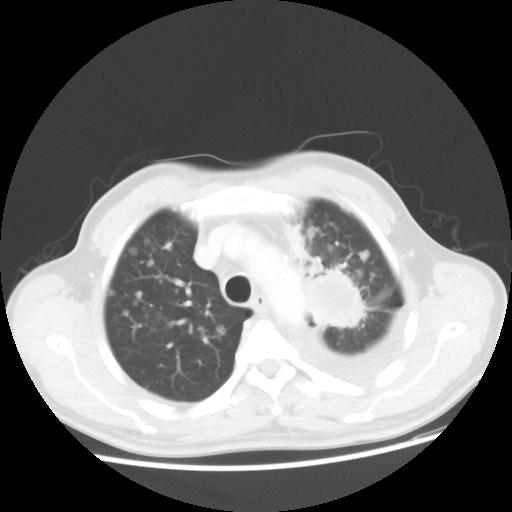
Chest CT, one axial slice. Position 37 of 48 along the scan axis. Reconstruction kernel STANDARD. 100 kVp. Lung window (W 1500 / L -600 HU). 5 mm slice thickness. 512 × 512 image matrix, field of view 362 × 362 mm. Patient: male, 55 years. From the clinical record (not read from this slice): clinical TNM (as recorded): T2 N3 M1a.
Outlined on this slice (rectangle marked by the reading radiologist):
- lung tumour (recorded histology: squamous cell carcinoma): bounding box (x1, y1, x2, y2) in pixels: (303, 268, 375, 351)